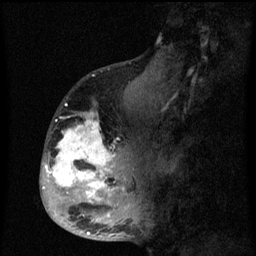
Breast MRI (dynamic contrast-enhanced), one sagittal slice. Dynamic contrast-enhanced series, image 2 of 3 at this slice position (ordered by acquisition). 1.5 T. TE 4.2 ms, TR 8 ms. 2 mm slice thickness. 256 × 256 image matrix, field of view 190 × 190 mm. Female patient, age 50 years.
Structures marked on this image (semi-automatically segmented with operator editing):
- analysis volume of interest (the breast-tissue region the enhancement analysis was run in; not a lesion): bounding box <43,90,142,216> (left, top, right, bottom; pixels)
- tumour enhancement mask (voxels above the 70 % enhancement threshold inside the analysis volume of interest): <43,112,124,216>